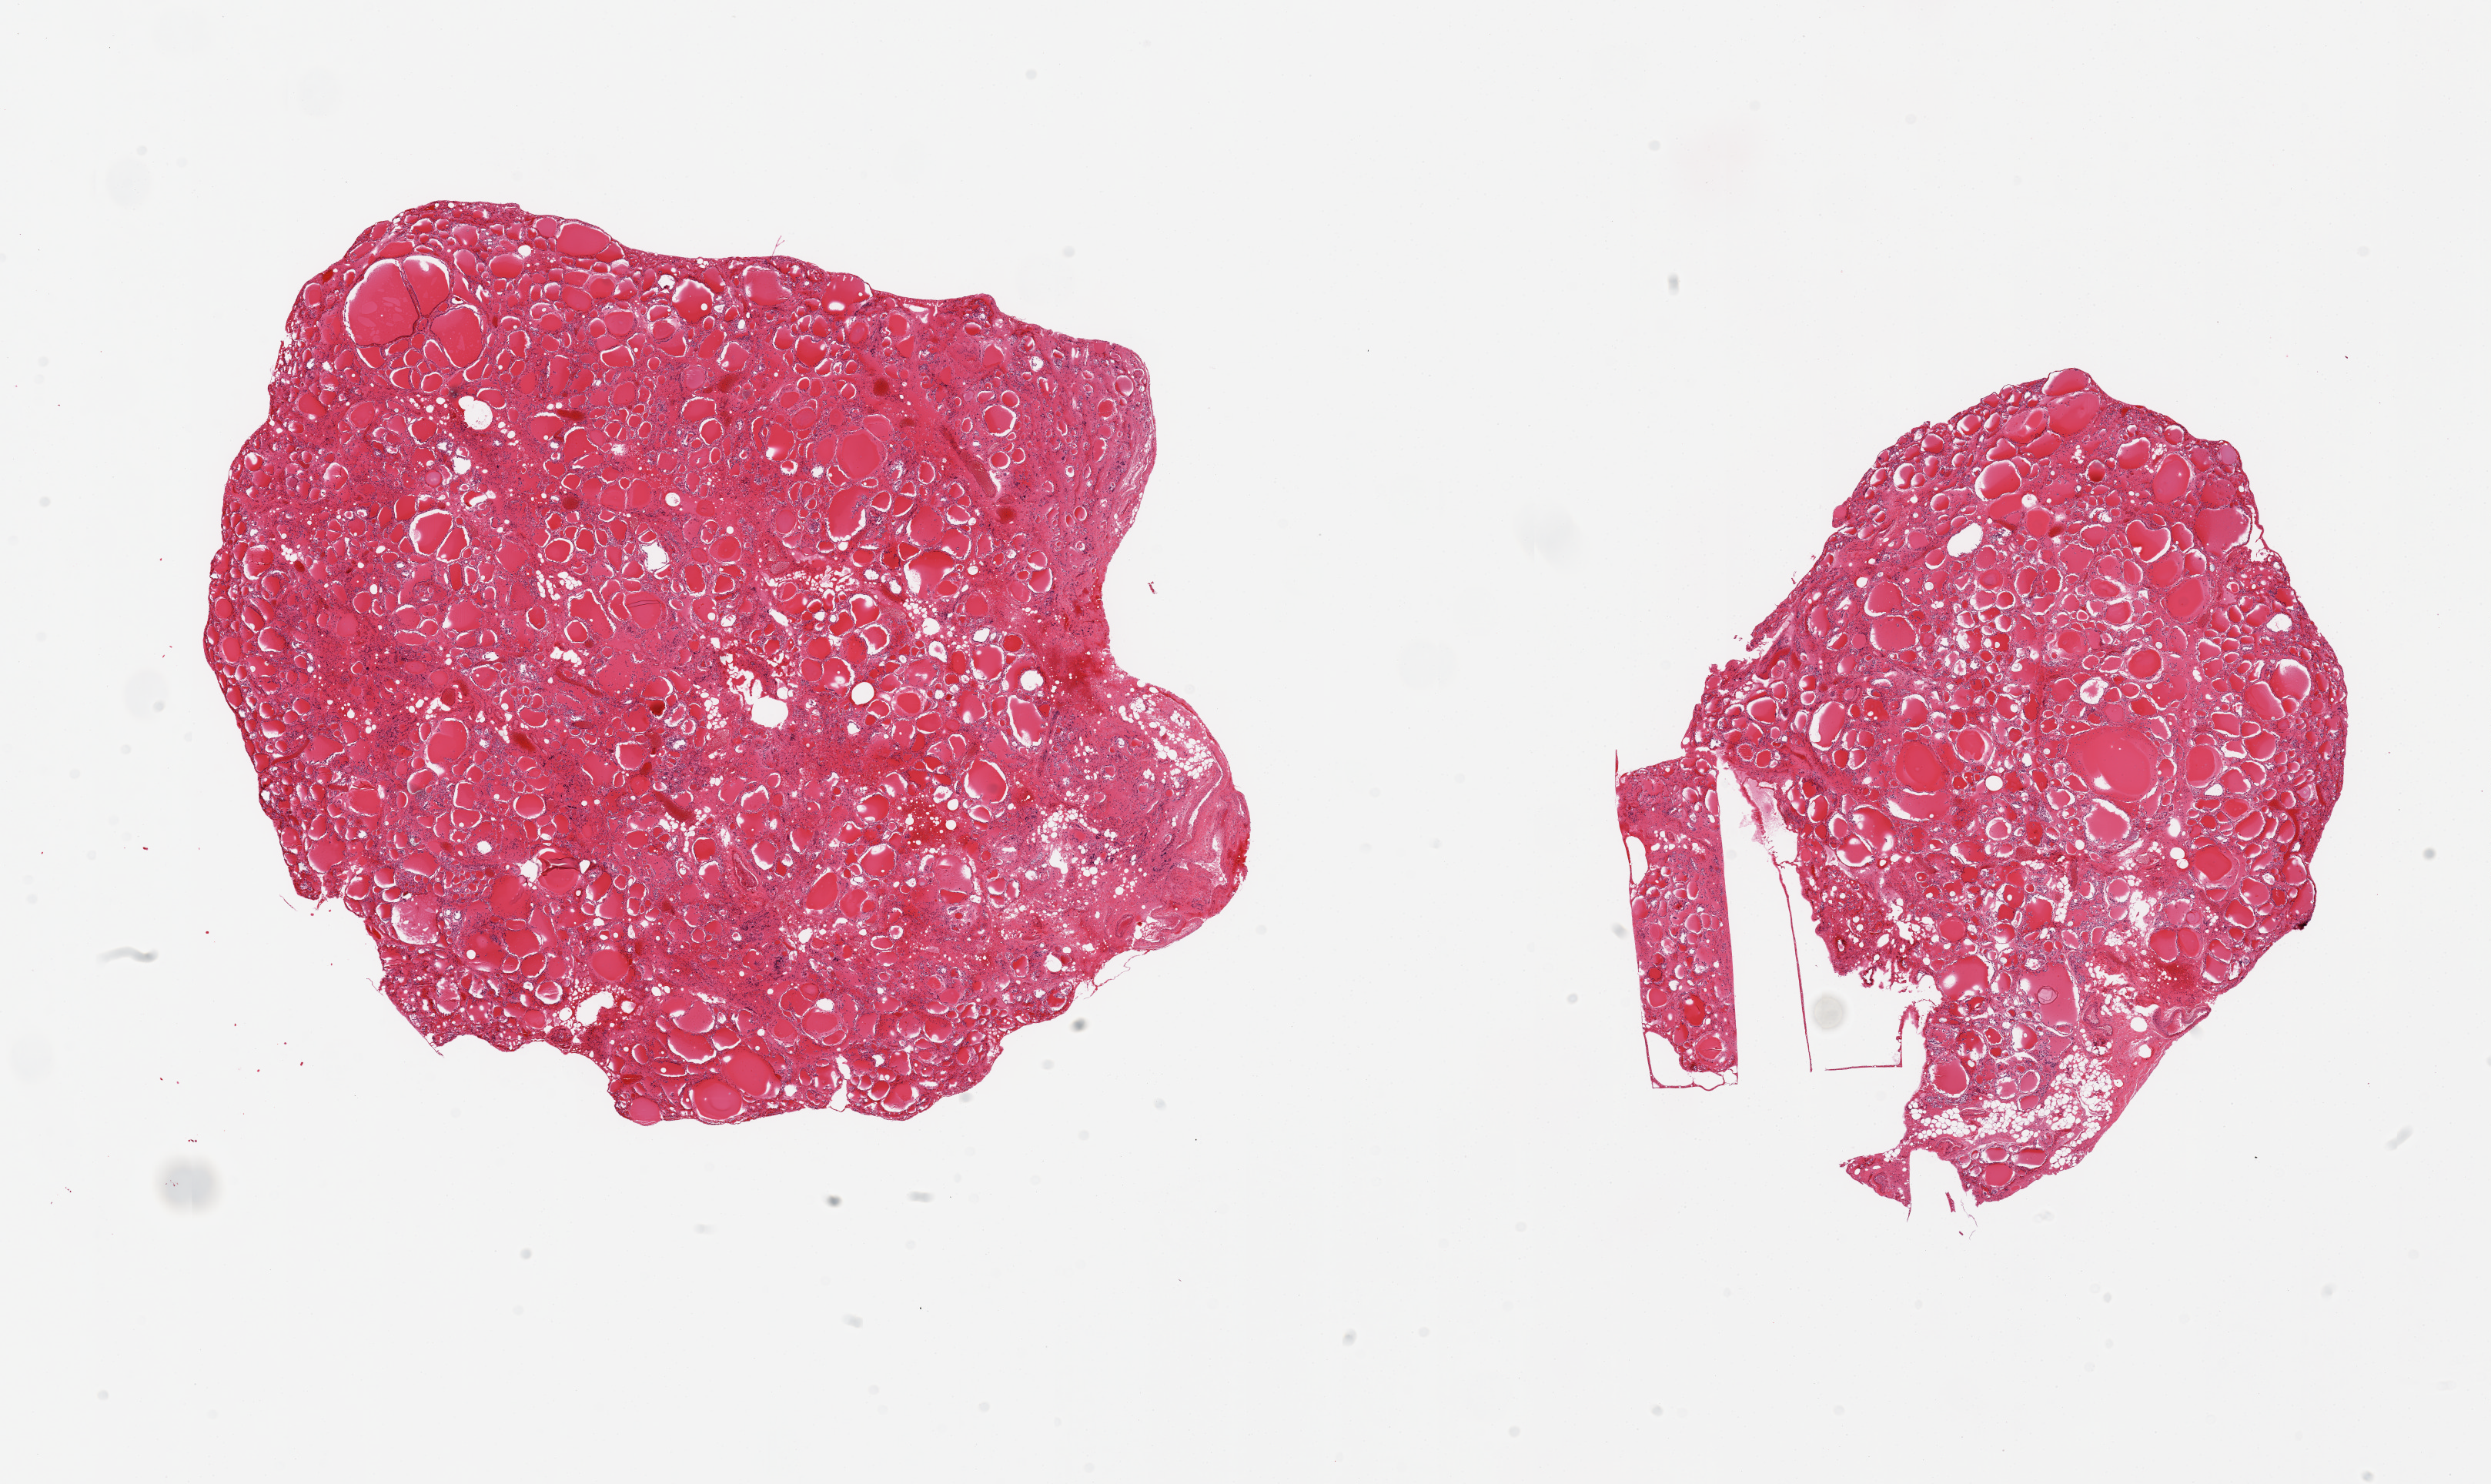
Digitized haematoxylin and eosin-stained section, brightfield — whole scanned area (about 25.6 x 15.2 mm) shown as a low-resolution overview, PAXgene-fixed, paraffin-embedded tissue, sampled site (target tissue): thyroid, donor tissue sample. Donor sex: male.
* pathologist's review note for this sample: 2 pieces, minute colloid cyst, no abnormalities